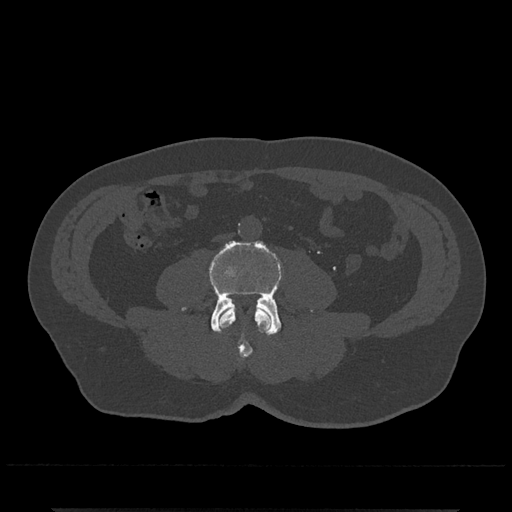
CT including the spine, one axial slice; position 179 of 797 along the scan axis; bone window (W 1800 / L 400 HU); 0.5 mm slice thickness; 512 × 512 image matrix, field of view 393 × 393 mm. Patient: male, 67 years. Case-level facts recorded for this patient, not image findings: primary cancer: prostate.
Annotated regions visible in this slice (semi-automatically segmented with operator editing):
- L3 vertebra: box from (x=219, y=307) to (x=272, y=358) px
- L4 vertebra: (x=182, y=240)–(x=284, y=336)